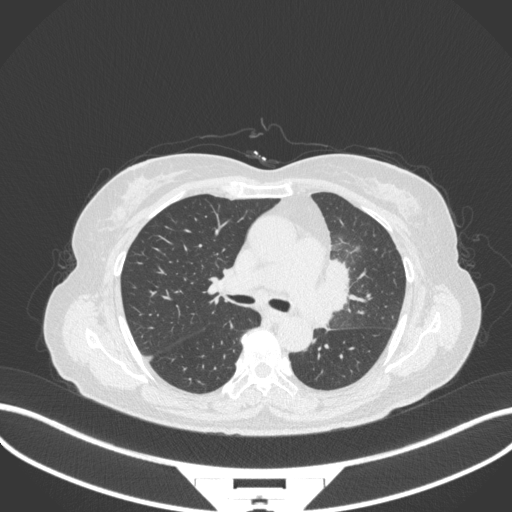
Chest CT, one axial slice; slice 206 of 382 in the series (ordered by position); 120 kVp; lung window (W 1500 / L -600 HU); 1 mm slice thickness; 512 × 512 image matrix. Female patient, age 64 years. From the clinical record (not read from this slice): clinical TNM (as recorded): T2a N2 M0.
Annotated regions visible in this slice (bounding box drawn by a radiologist):
- lung tumour (recorded histology: adenocarcinoma): box from (x=316, y=253) to (x=358, y=335) px